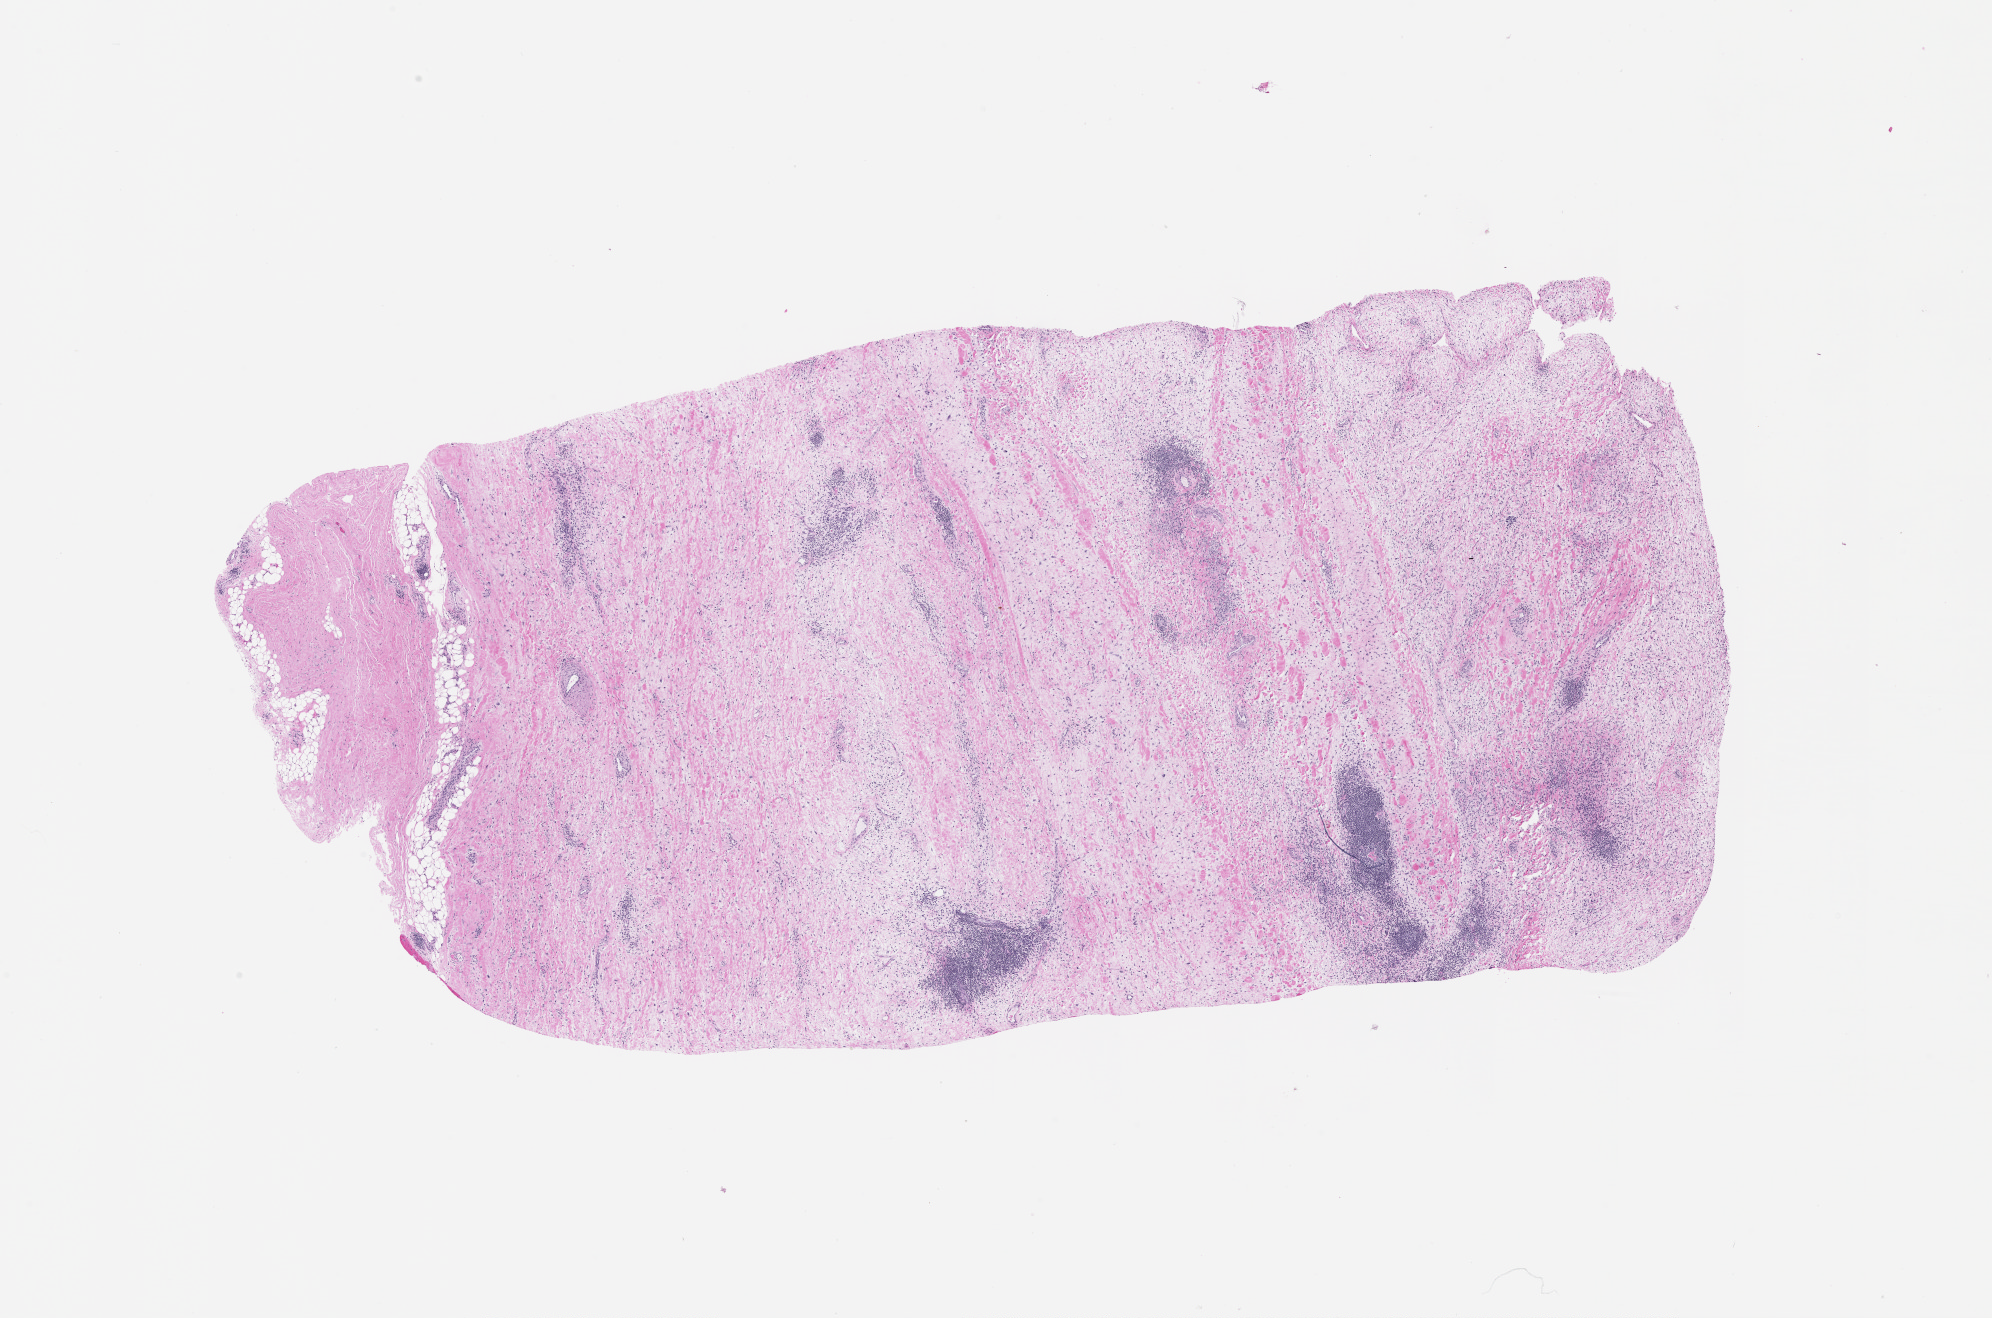
Whole-slide histology image, H&E-stained, shown as a low-resolution overview of the whole scanned area (about 16.0 x 10.6 mm, slide scanned at 20x).
Patient diagnosis (cohort enrolment): sarcoma (site not recorded at cohort level).